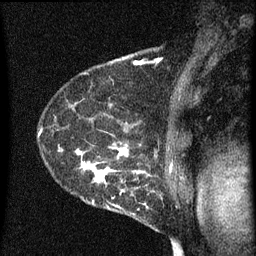
Breast MRI (dynamic contrast-enhanced), one sagittal slice; position 48 of 60 along the scan axis; dynamic contrast-enhanced series, image 2 of 3 at this slice position (ordered by acquisition); 1.5 T; TE 4.2 ms, TR 8 ms; 2 mm slice thickness; 256 × 256 image matrix, field of view 180 × 180 mm. Patient: female, 54 years.
Structures marked on this image (semi-automatically segmented with operator editing):
- analysis volume of interest (the breast-tissue region the enhancement analysis was run in; not a lesion): bounding box (x1, y1, x2, y2) in pixels: (49, 138, 164, 209)
- tumour enhancement mask (voxels above the 70 % enhancement threshold inside the analysis volume of interest): (59, 142, 149, 209)